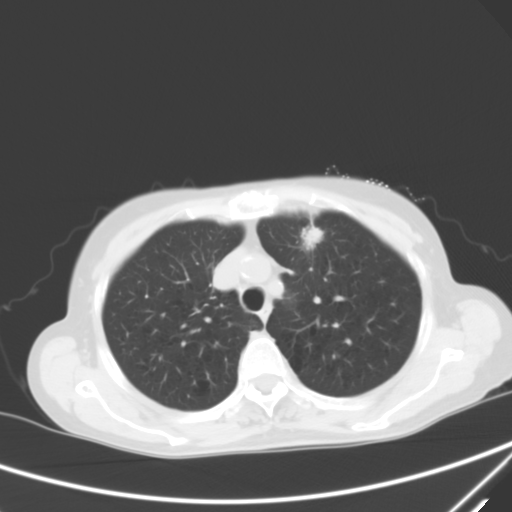
Chest CT, one axial slice. Slice 47 of 60 in the series (ordered by position). Lung window (W 1500 / L -600 HU). 5 mm slice thickness. 512 × 512 image matrix, field of view 350 × 350 mm. Patient: female, 71 years. From the clinical record (not read from this slice): clinical TNM (as recorded): T1c N0 M0; histopathological grade: G2-3.
Annotated regions visible in this slice (rectangle marked by the reading radiologist):
- lung tumour (recorded histology: adenocarcinoma): bounding box (x1, y1, x2, y2) in pixels: (298, 222, 328, 251)